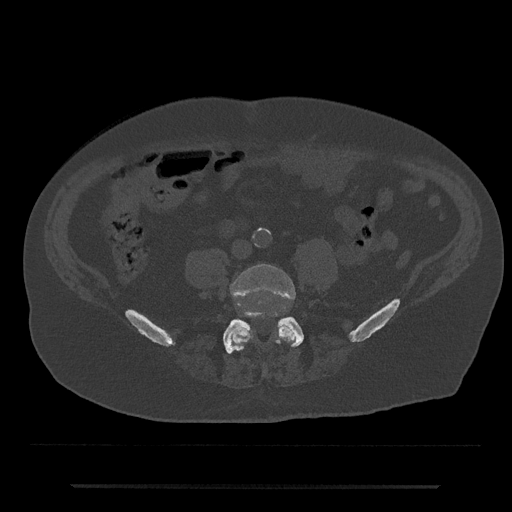
CT including the spine, one axial slice. Slice 318 of 797 in the series (ordered by position). 120 kVp. Bone window (W 1800 / L 400 HU). 0.5 mm slice thickness. 512 × 512 image matrix. Male patient, age 80 years. Case-level facts recorded for this patient, not image findings: primary cancer: prostate; vertebrae with lytic lesions (as recorded): L1, T11.
Outlined on this slice (semi-automatic segmentation, software-assisted and operator-edited):
- L4 vertebra: bounding box (x1, y1, x2, y2) in pixels: (230, 264, 296, 349)
- L5 vertebra: (223, 311, 304, 354)